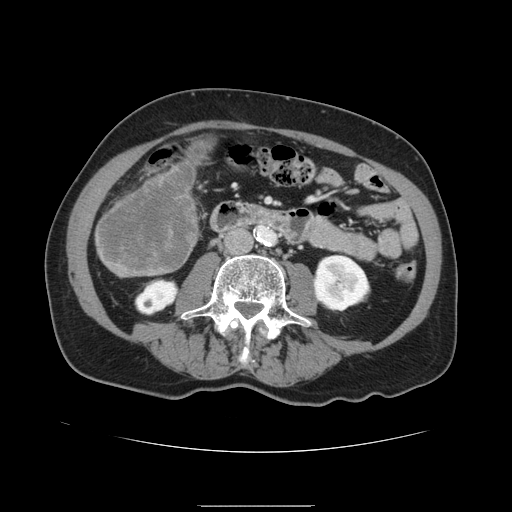
Contrast-enhanced abdominal CT, one axial slice; slice 30 of 168 in the series (ordered by position); 120 kVp; intravenous contrast given; soft-tissue window (W 400 / L 40 HU); 2.5 mm slice thickness; 512 × 512 image matrix, field of view 386 × 386 mm. Male patient, age 74 years. From the clinical record (not read from this slice): diagnosis: colorectal cancer liver metastases, imaged before liver resection; multiple liver metastases: no; largest metastasis: 14.5 cm; disease in both lobes: yes.
Structures marked on this image (manually delineated by an expert):
- liver: box from (x=94, y=141) to (x=210, y=277) px
- liver metastasis: (x=98, y=146)–(x=205, y=274)